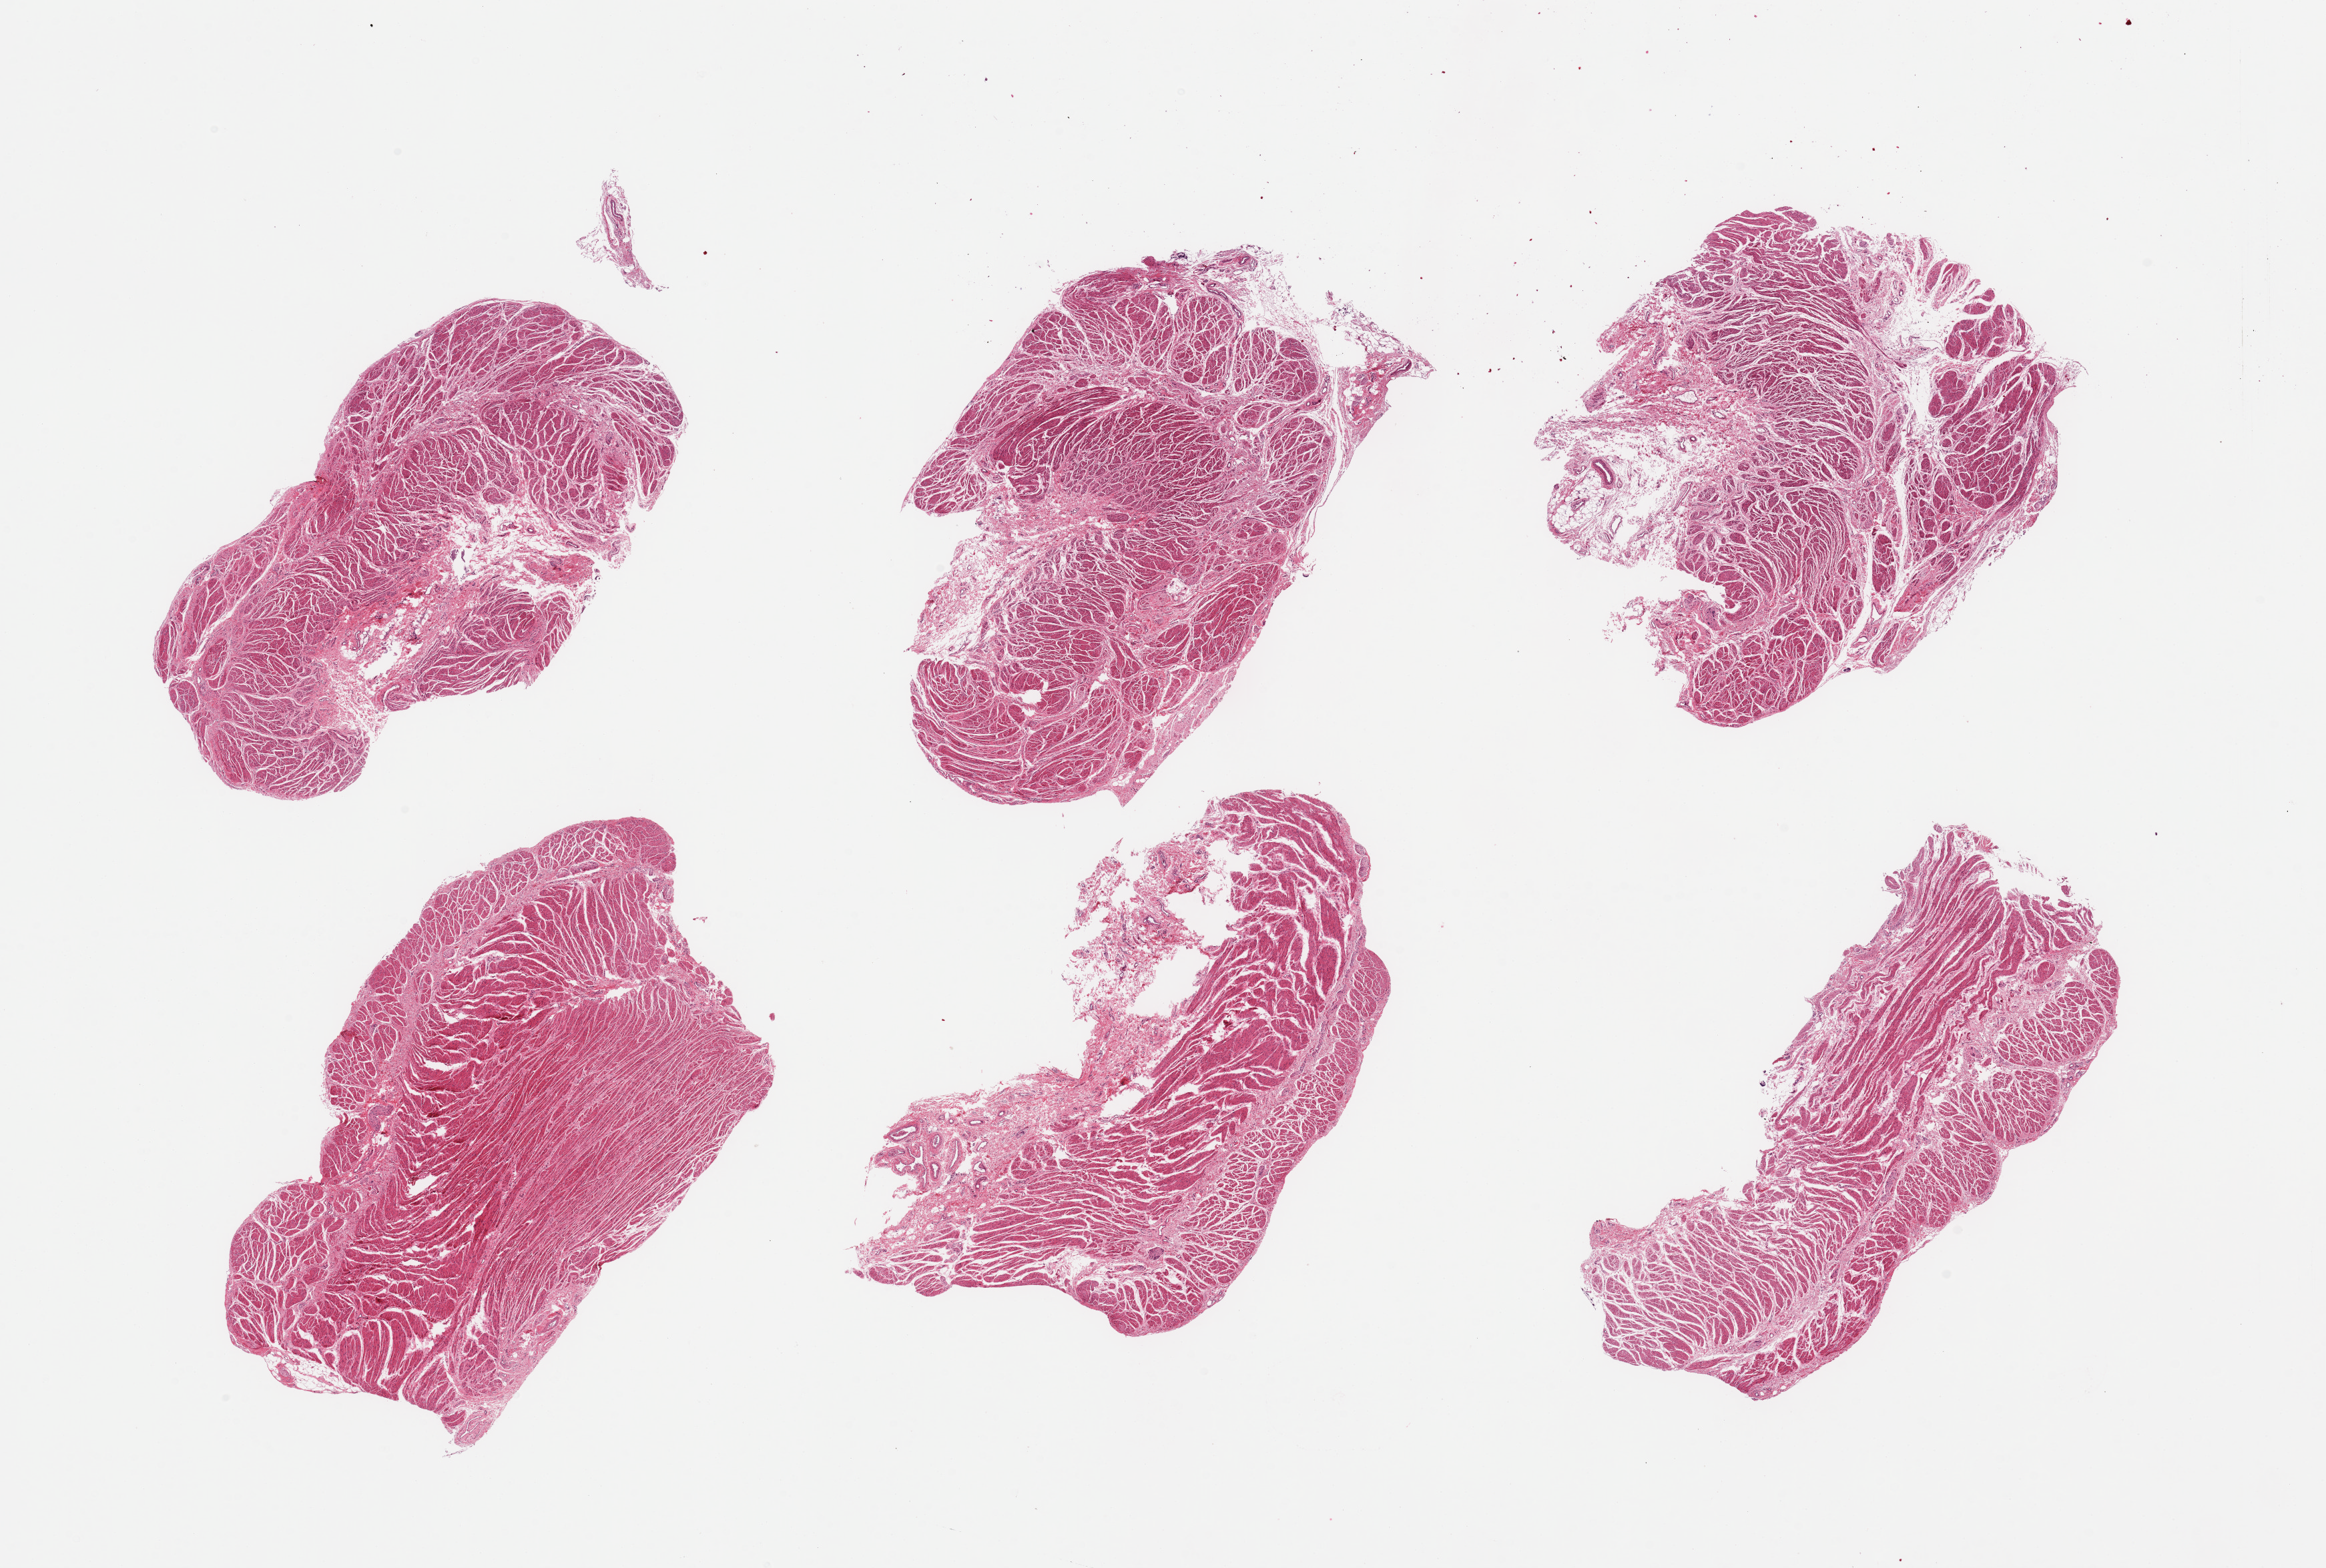
Whole-slide image, haematoxylin and eosin stain, low-resolution overview of the scanned area, about 27.6 x 18.6 mm. PAXgene-fixed, paraffin-embedded tissue. Sampled site (target tissue): gastroesophageal junction. Donor tissue sample. Female donor.
* review note (as recorded): 6 pieces; muscularis with variable amounts of submucosa